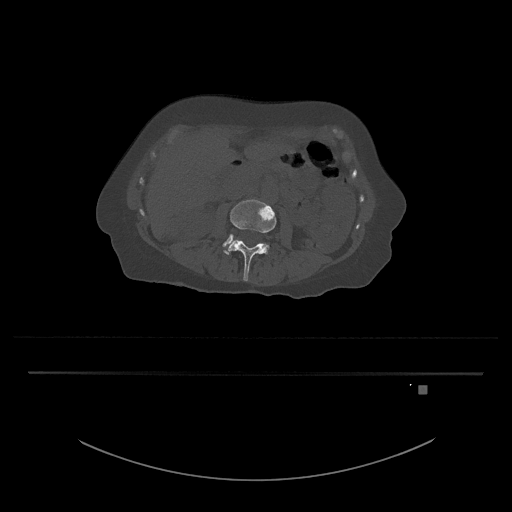
CT including the spine, one axial slice. Slice 417 of 797 in the series (ordered by position). Bone window (W 1800 / L 400 HU). 0.5 mm slice thickness. 512 × 512 image matrix, field of view 500 × 500 mm. Patient: female, 57 years. Case-level facts recorded for this patient, not image findings: primary cancer: cervical.
Outlined on this slice (semi-automatically segmented with operator editing):
- L3 vertebra: bounding box [x1, y1, x2, y2] px = [224, 200, 277, 281]
- L4 vertebra: [223, 234, 233, 247]